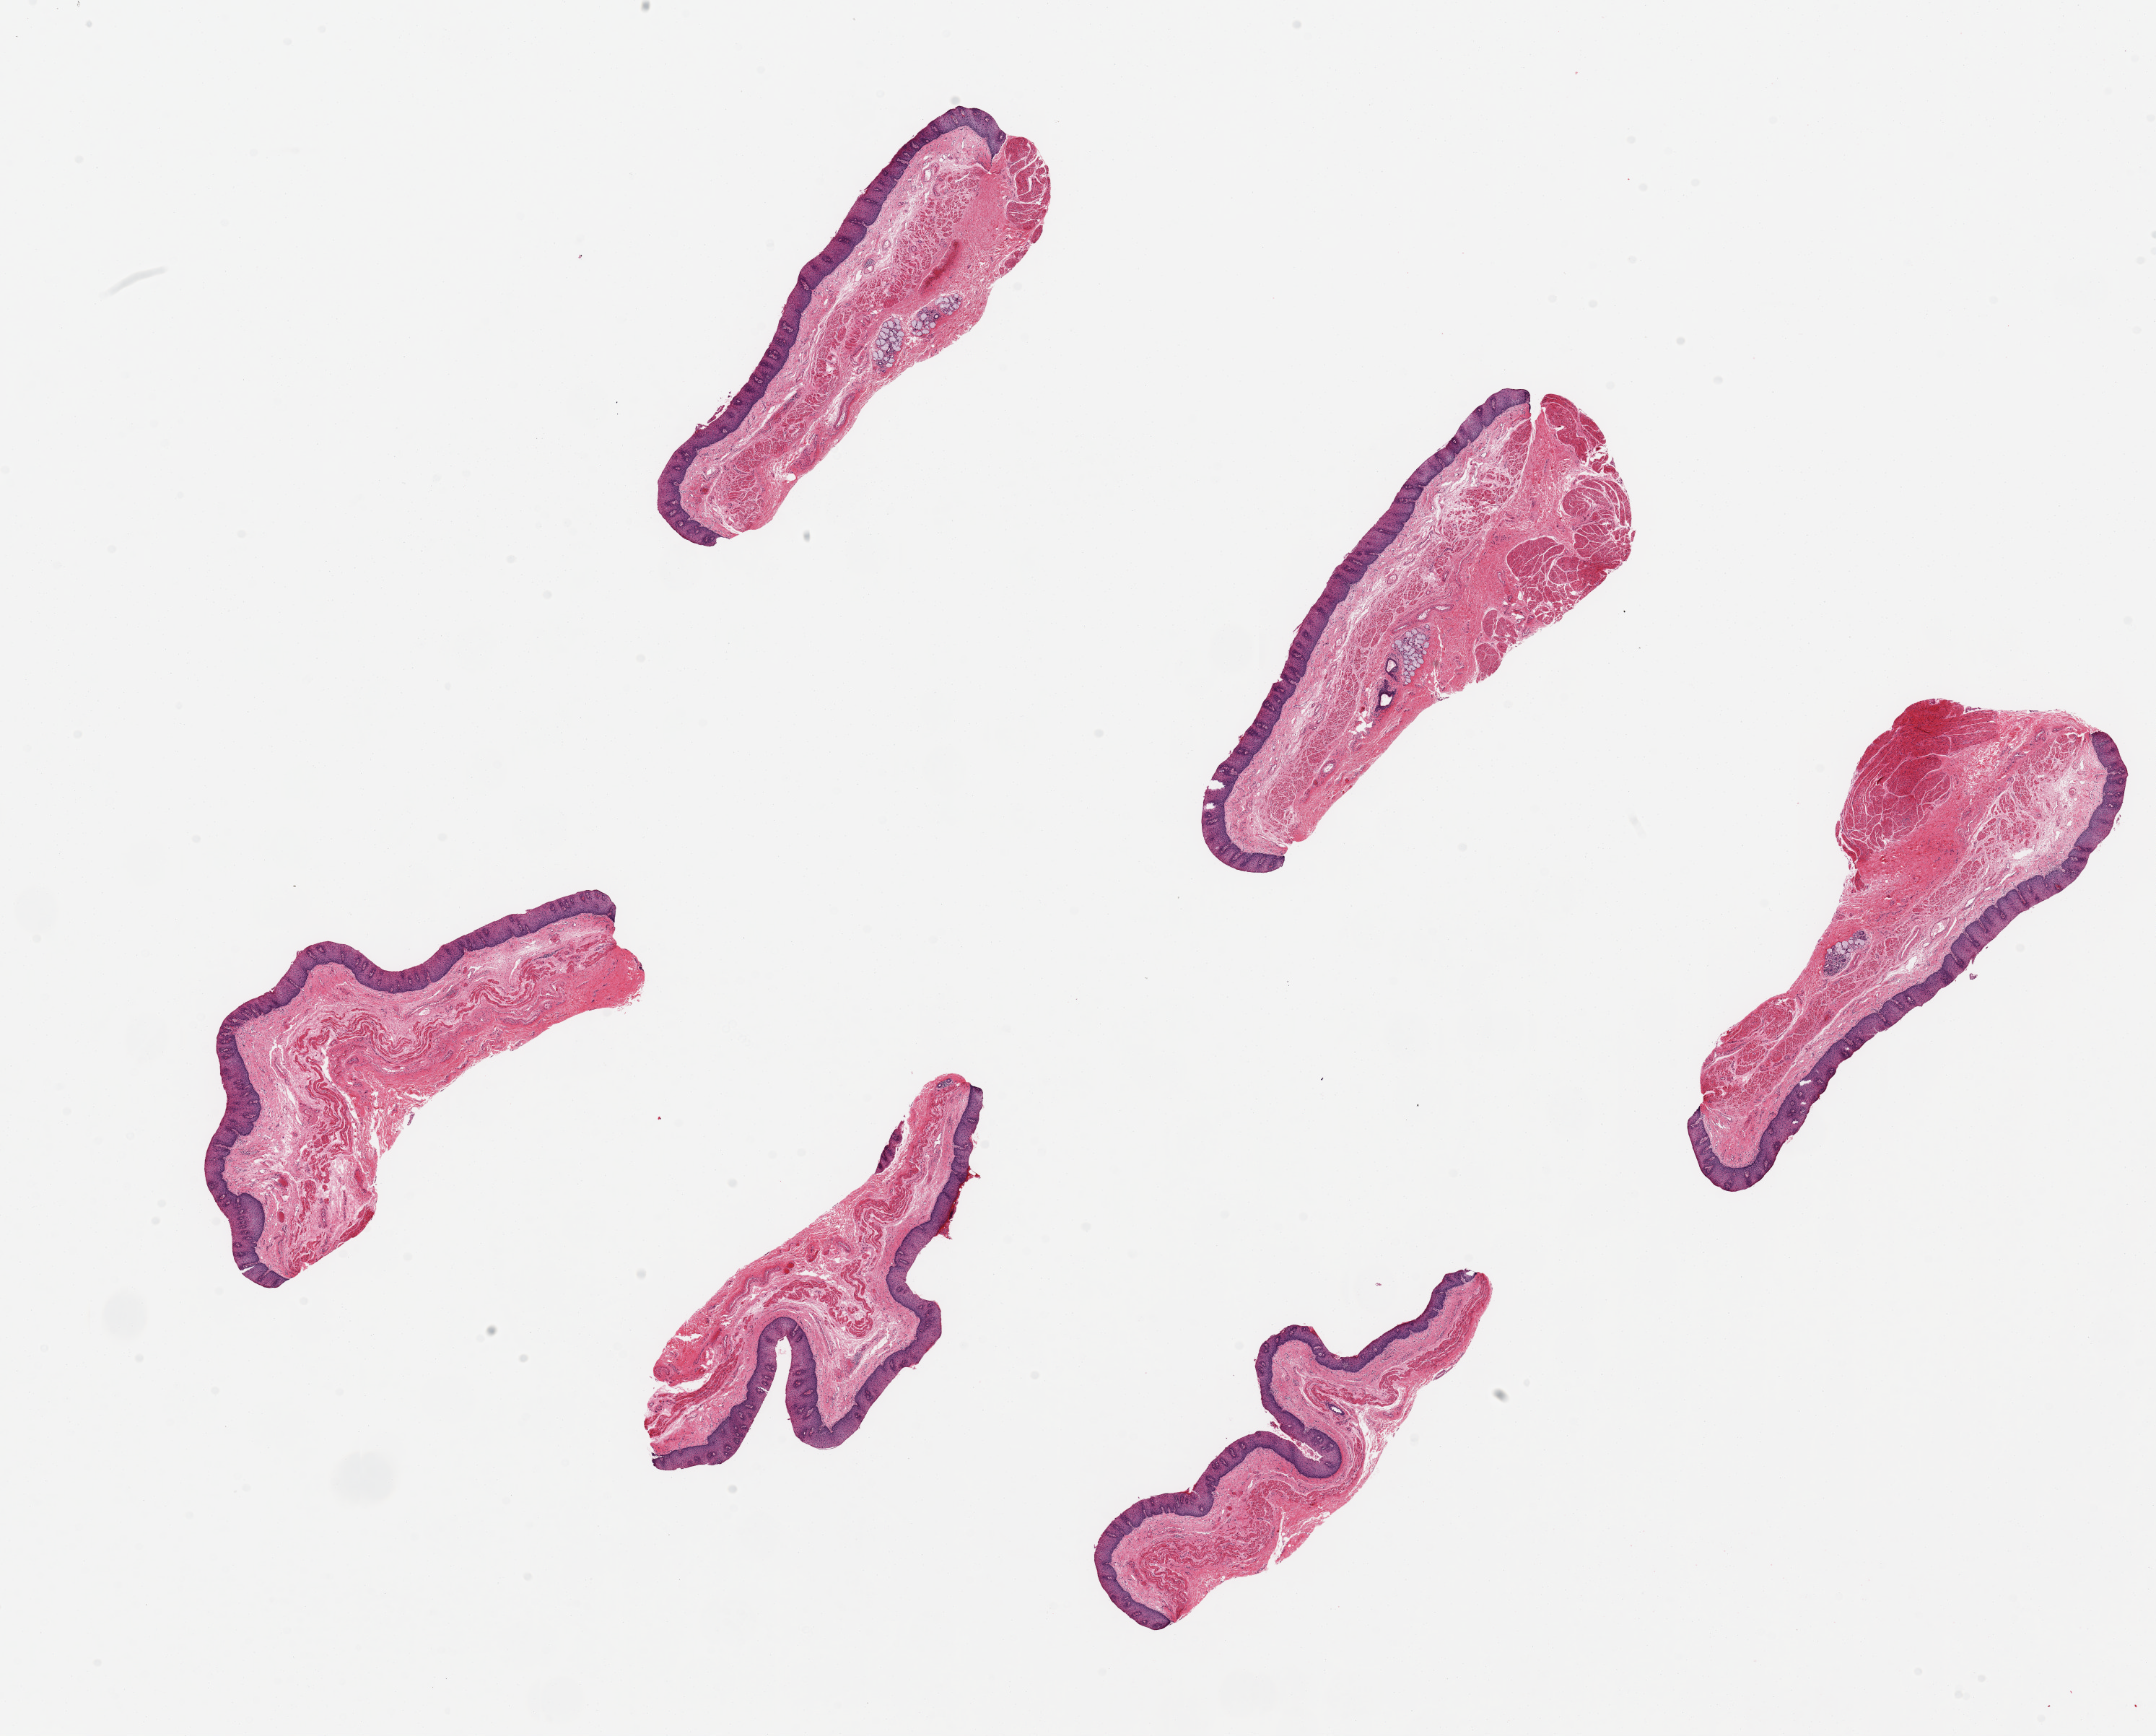
Digitized H&E-stained section, brightfield, a low-resolution overview of the entire scanned area, about 23.6 x 19.0 mm (acquisition: 20x scan); PAXgene-fixed, paraffin-embedded tissue; target tissue: esophageal mucous membrane; tissue donor sample. Donor sex: male.
Pathologist's review note for this sample: 6 pieces up to 6x2.5 mm; 3 have up to 1 x2 mm muscularis propria at edge.